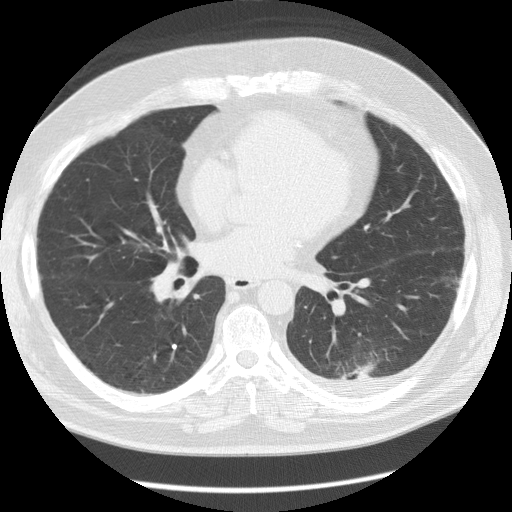
Low-dose screening chest CT, one axial slice; position 61 of 126 along the scan axis; reconstruction kernel STANDARD; 120 kVp; lung window (W 1500 / L -600 HU); 2.5 mm slice thickness; 512 × 512 image matrix.
Outlined on this slice (expert manual segmentation):
- lesion 1 (tumor, lower lobe of left lung): bounding box [x1, y1, x2, y2] px = [343, 364, 372, 380]